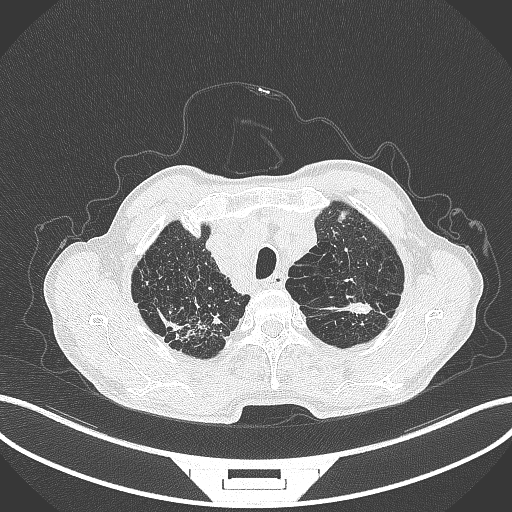
Chest CT, one axial slice. Slice 382 of 463 in the series (ordered by position). Reconstruction kernel B70f. Lung window (W 1500 / L -600 HU). 1 mm slice thickness. 512 × 512 image matrix. Patient: male, 74 years. Case-level facts recorded for this patient, not image findings: clinical TNM (as recorded): T2a N1 M0.
Structures marked on this image (bounding box drawn by a radiologist):
- lung tumour (recorded histology: adenocarcinoma): bounding box [x1, y1, x2, y2] px = [330, 296, 376, 319]